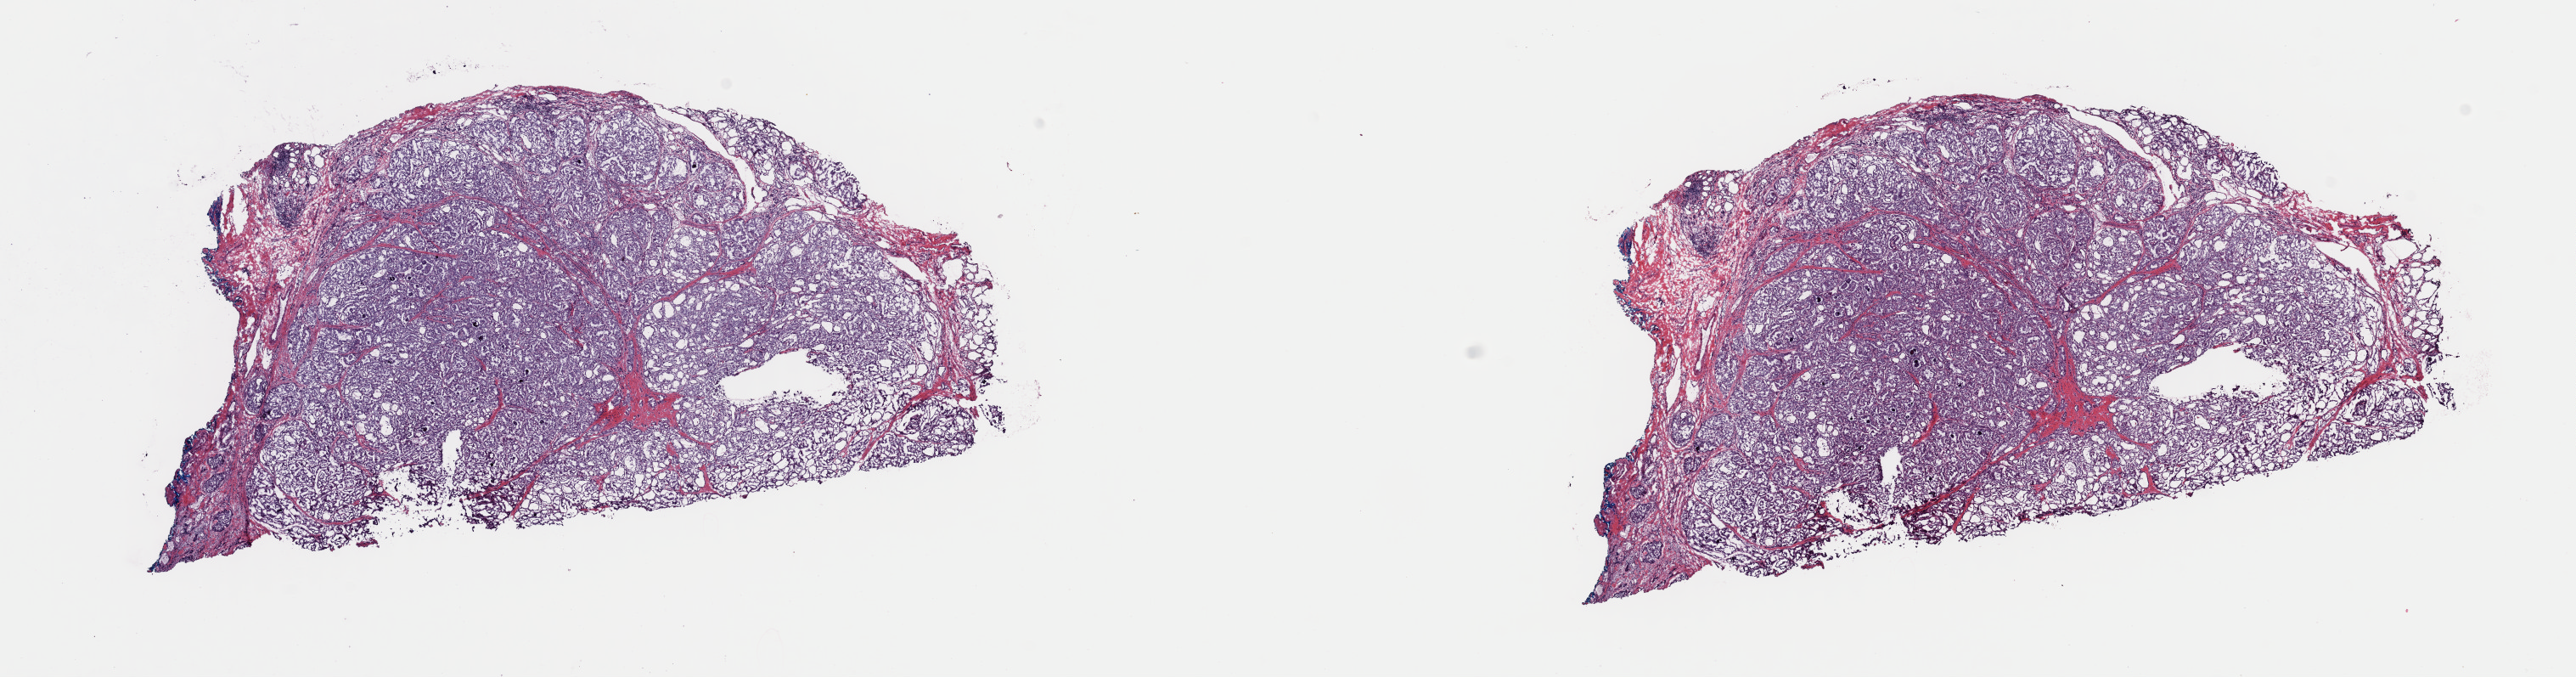
Digitized H&E tissue section (whole slide) — whole scanned area (about 24.0 x 6.3 mm, from a 40x scan) shown as a low-resolution overview, frozen section from the top of the tissue portion, sample: primary tumour, thyroid. Female, age 15 years at initial diagnosis. Slide review estimates, as recorded: tumour cells 80%, tumour nuclei 95%, normal cells 5%, stromal cells 15%, necrosis 0%. Infiltration values recorded for this section: lymphocyte infiltration 1%, monocyte infiltration 1%, neutrophil infiltration 0%.
Laterality: right. Lymph nodes positive (case pathology): 5 of 49 examined. TNM: T1b N1b M0. Histologic diagnosis: Papillary adenocarcinoma, NOS (thyroid gland). AJCC pathologic stage: I (7th edition).